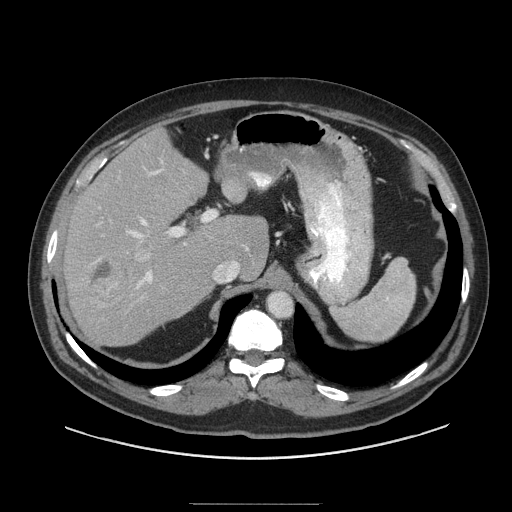
Contrast-enhanced abdominal CT (liver protocol), one axial slice. Position 66 of 91 along the scan axis. Reconstruction kernel STANDARD. 140 kVp. Soft-tissue window (W 400 / L 40 HU). 512 × 512 image matrix, field of view 440 × 440 mm. Case-level facts recorded for this patient, not image findings: diagnosis: hepatocellular carcinoma (patient treated with transarterial chemoembolisation; whether this scan precedes or follows treatment is not stated here); TNM stage (as recorded): Stage-I; Child-Pugh class: A.
Outlined on this slice (semi-automatically segmented with operator editing):
- liver parenchyma outside the tumour (the mass and vessels are separate outlines, so this box may not span the whole liver): bounding box (x1, y1, x2, y2) in pixels: (62, 128, 268, 346)
- mass: (84, 259, 128, 299)
- liver vessels: (98, 170, 249, 289)